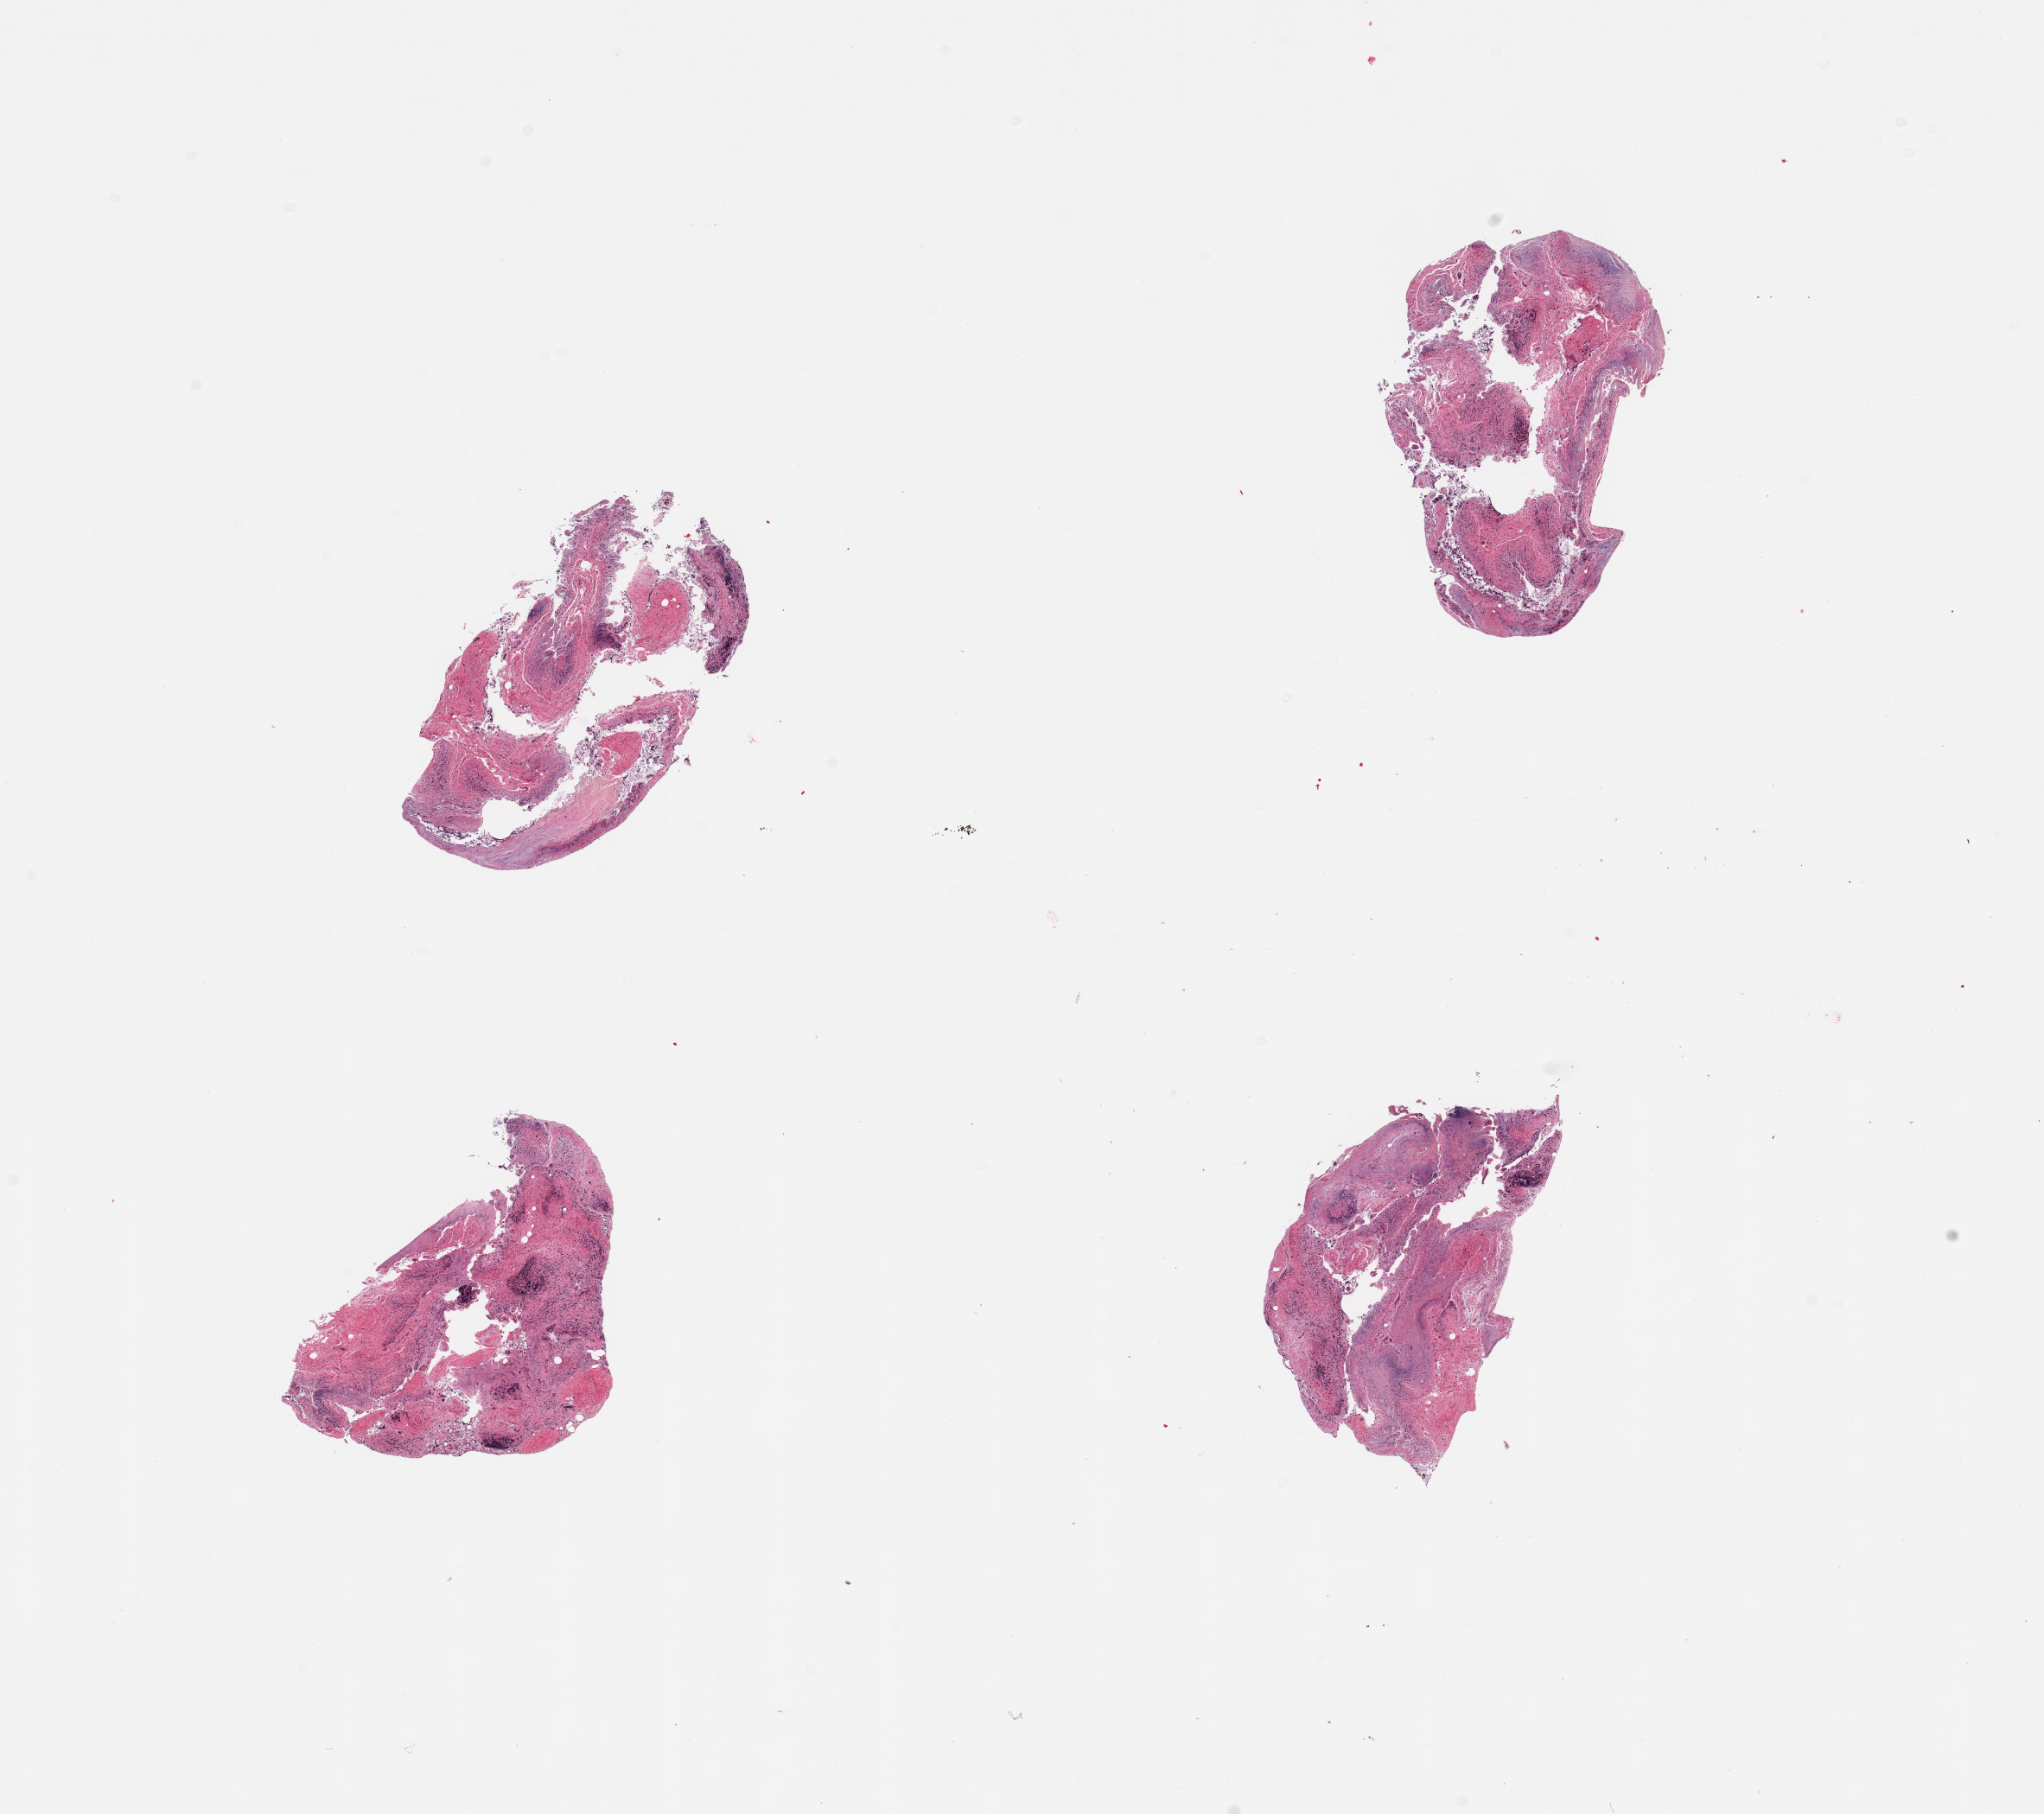
H&E whole-slide image — whole scanned area (about 18.7 x 16.6 mm) shown as a low-resolution overview; PAXgene-fixed, paraffin-embedded tissue; sampled site (target tissue): ileum; donor tissue sample. Female donor.
Pathologist's review note for this sample: 4 pieces. glandular mucosa completely autolyzed/sloughed; insufficient residual lymphoid aggregates to warrant attempted molecular analysis.